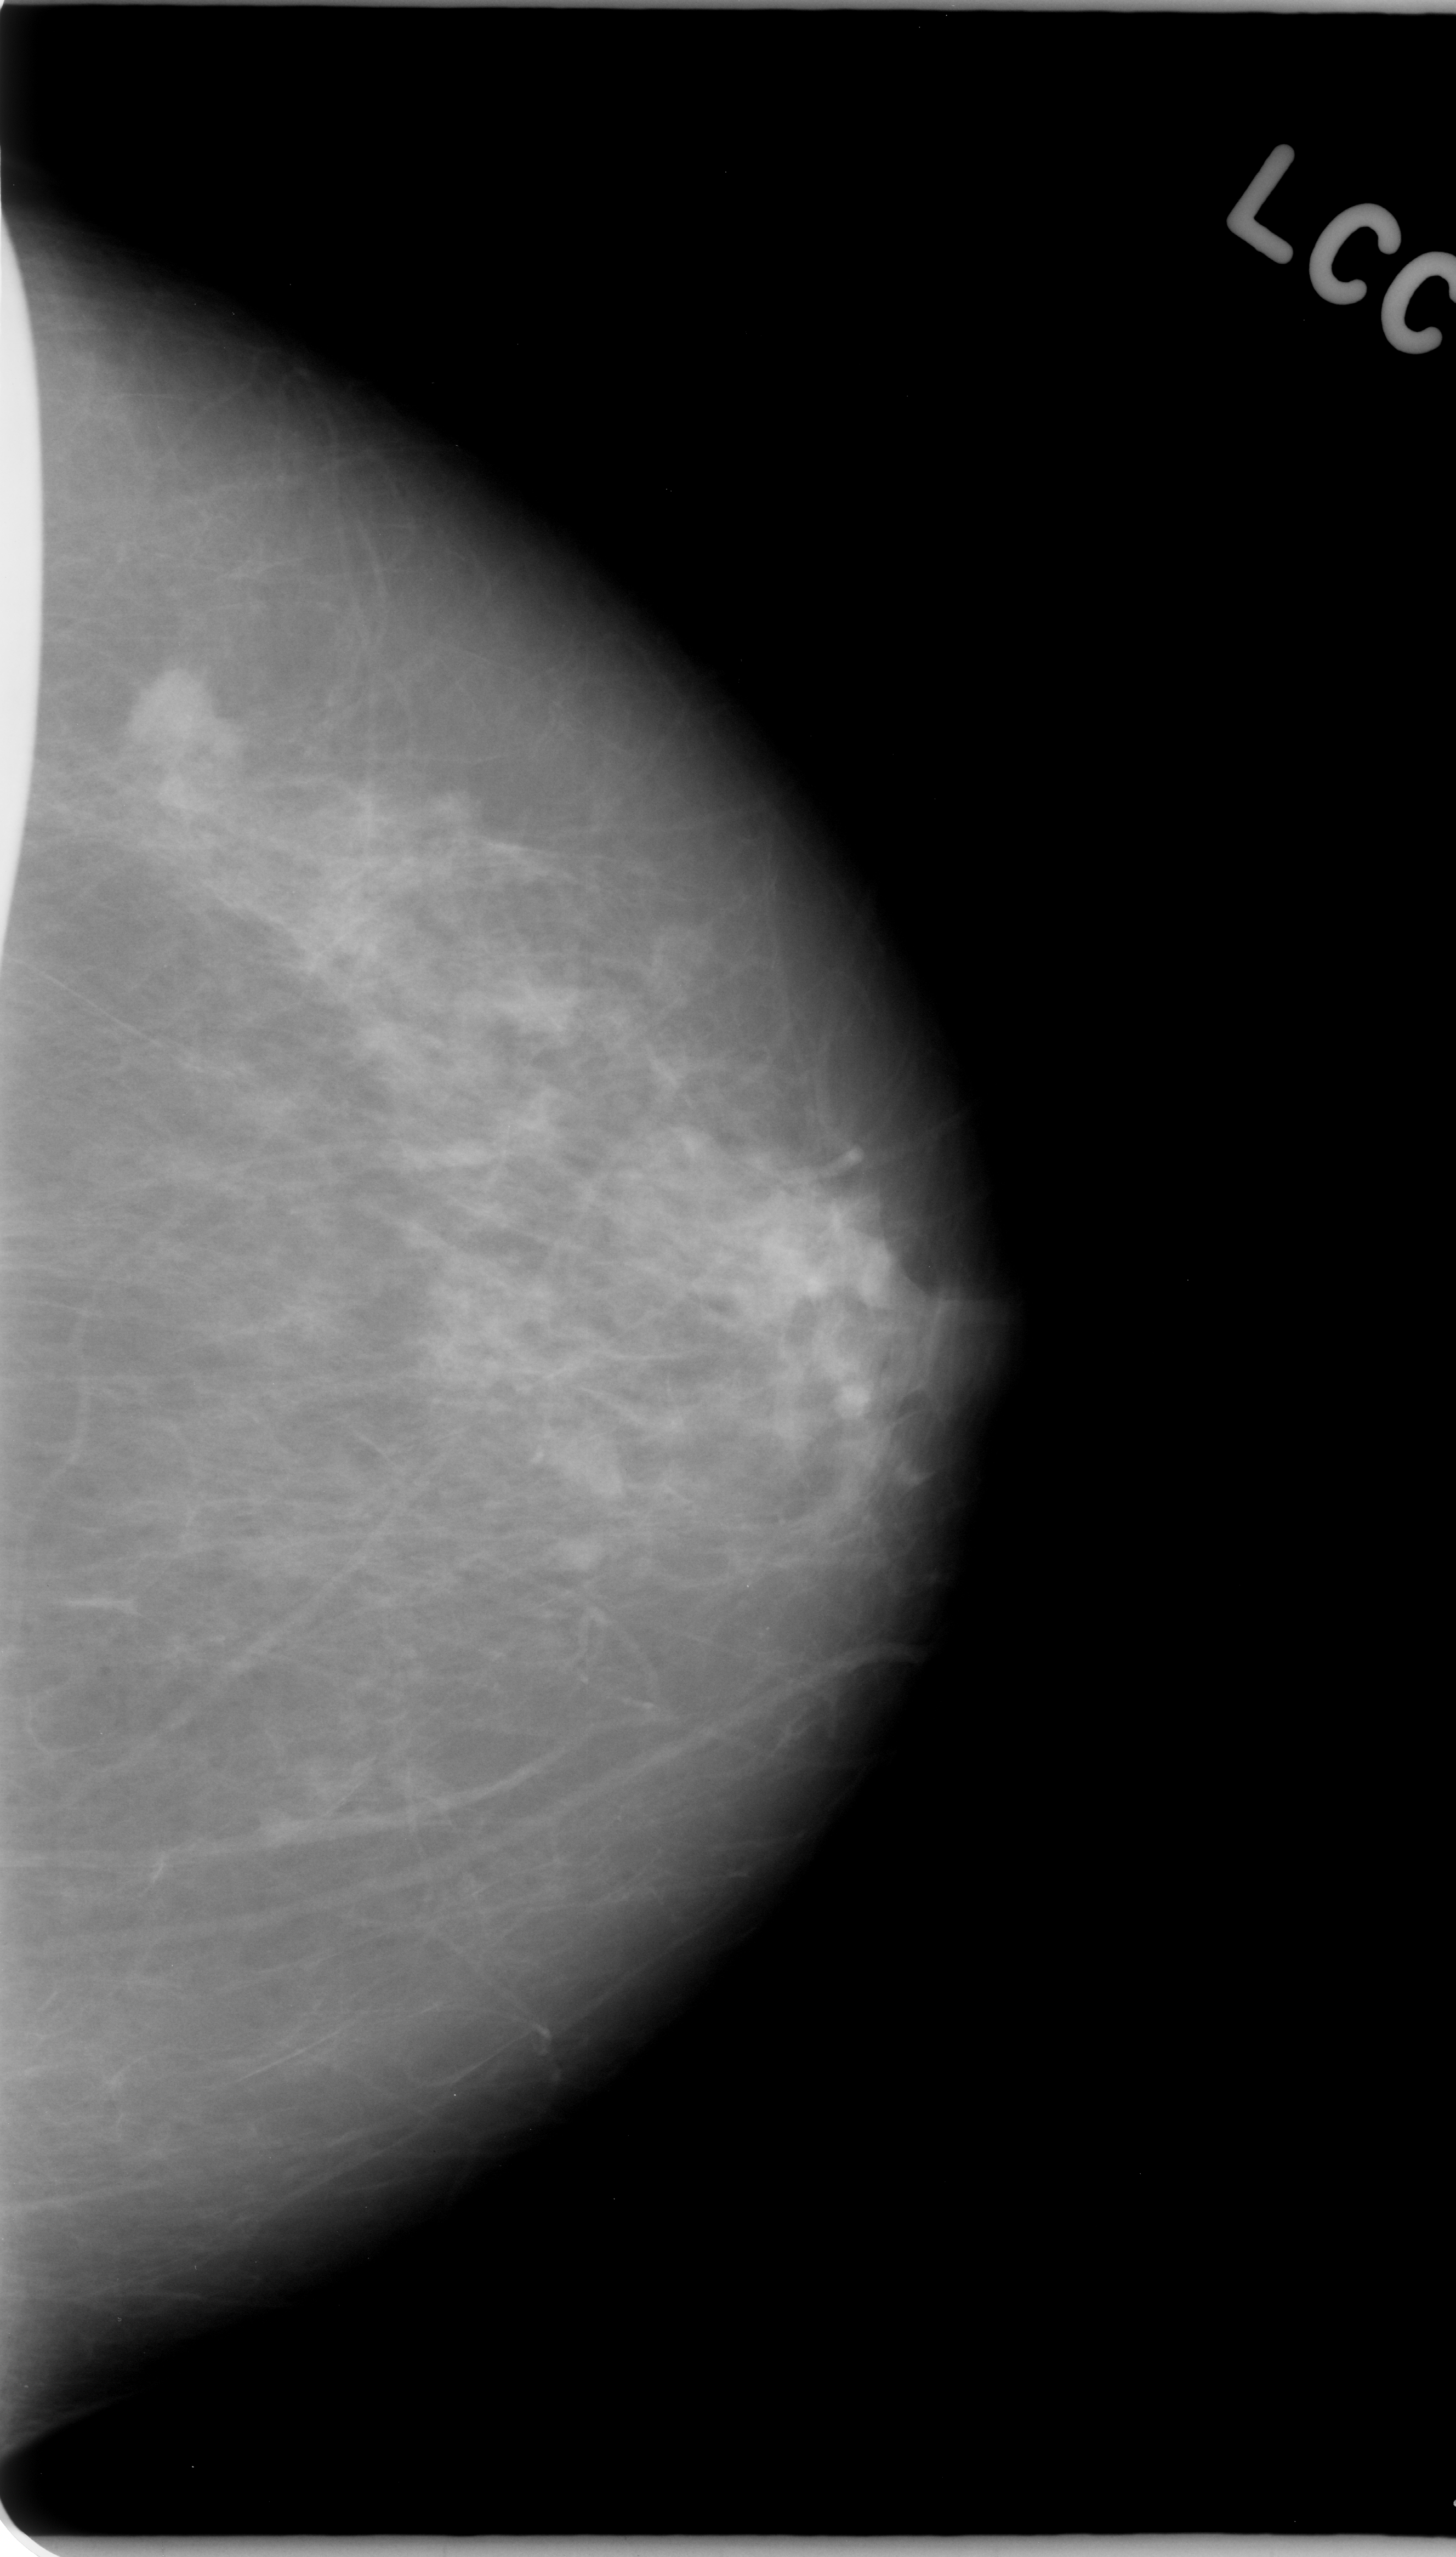
Mammogram (digitized film), left breast, CC view.
Marked findings (only marked abnormalities are described; nothing is implied about the rest of the image): mass, shape lobulated, margins microlobulated; BI-RADS assessment category 5; subtlety rating 5 on a 1 (subtle) to 5 (obvious) scale; pathology (as recorded): malignant.